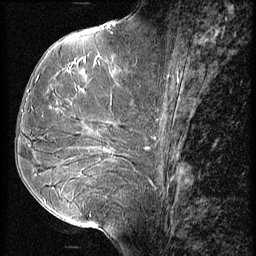
Breast MRI (dynamic contrast-enhanced), one sagittal slice. Position 29 of 56 along the scan axis. 3 images stored at this slice position (order not interpretable as contrast timing). 1.5 T. TE 4.2 ms, TR 9 ms. 256 × 256 image matrix, field of view 180 × 180 mm. Female patient, age 51 years. Case-level facts recorded for this patient, not image findings: setting: breast cancer imaged before/during neoadjuvant chemotherapy; receptor status: HR-positive, HER2-negative.
Annotated regions visible in this slice (semi-automatically segmented with operator editing):
- analysis volume of interest (the breast-tissue region the enhancement analysis was run in; not a lesion): bounding box <23,56,156,165> (left, top, right, bottom; pixels)
- tumour enhancement mask (voxels above the 140 % enhancement threshold inside the analysis volume of interest): <78,56,111,73>